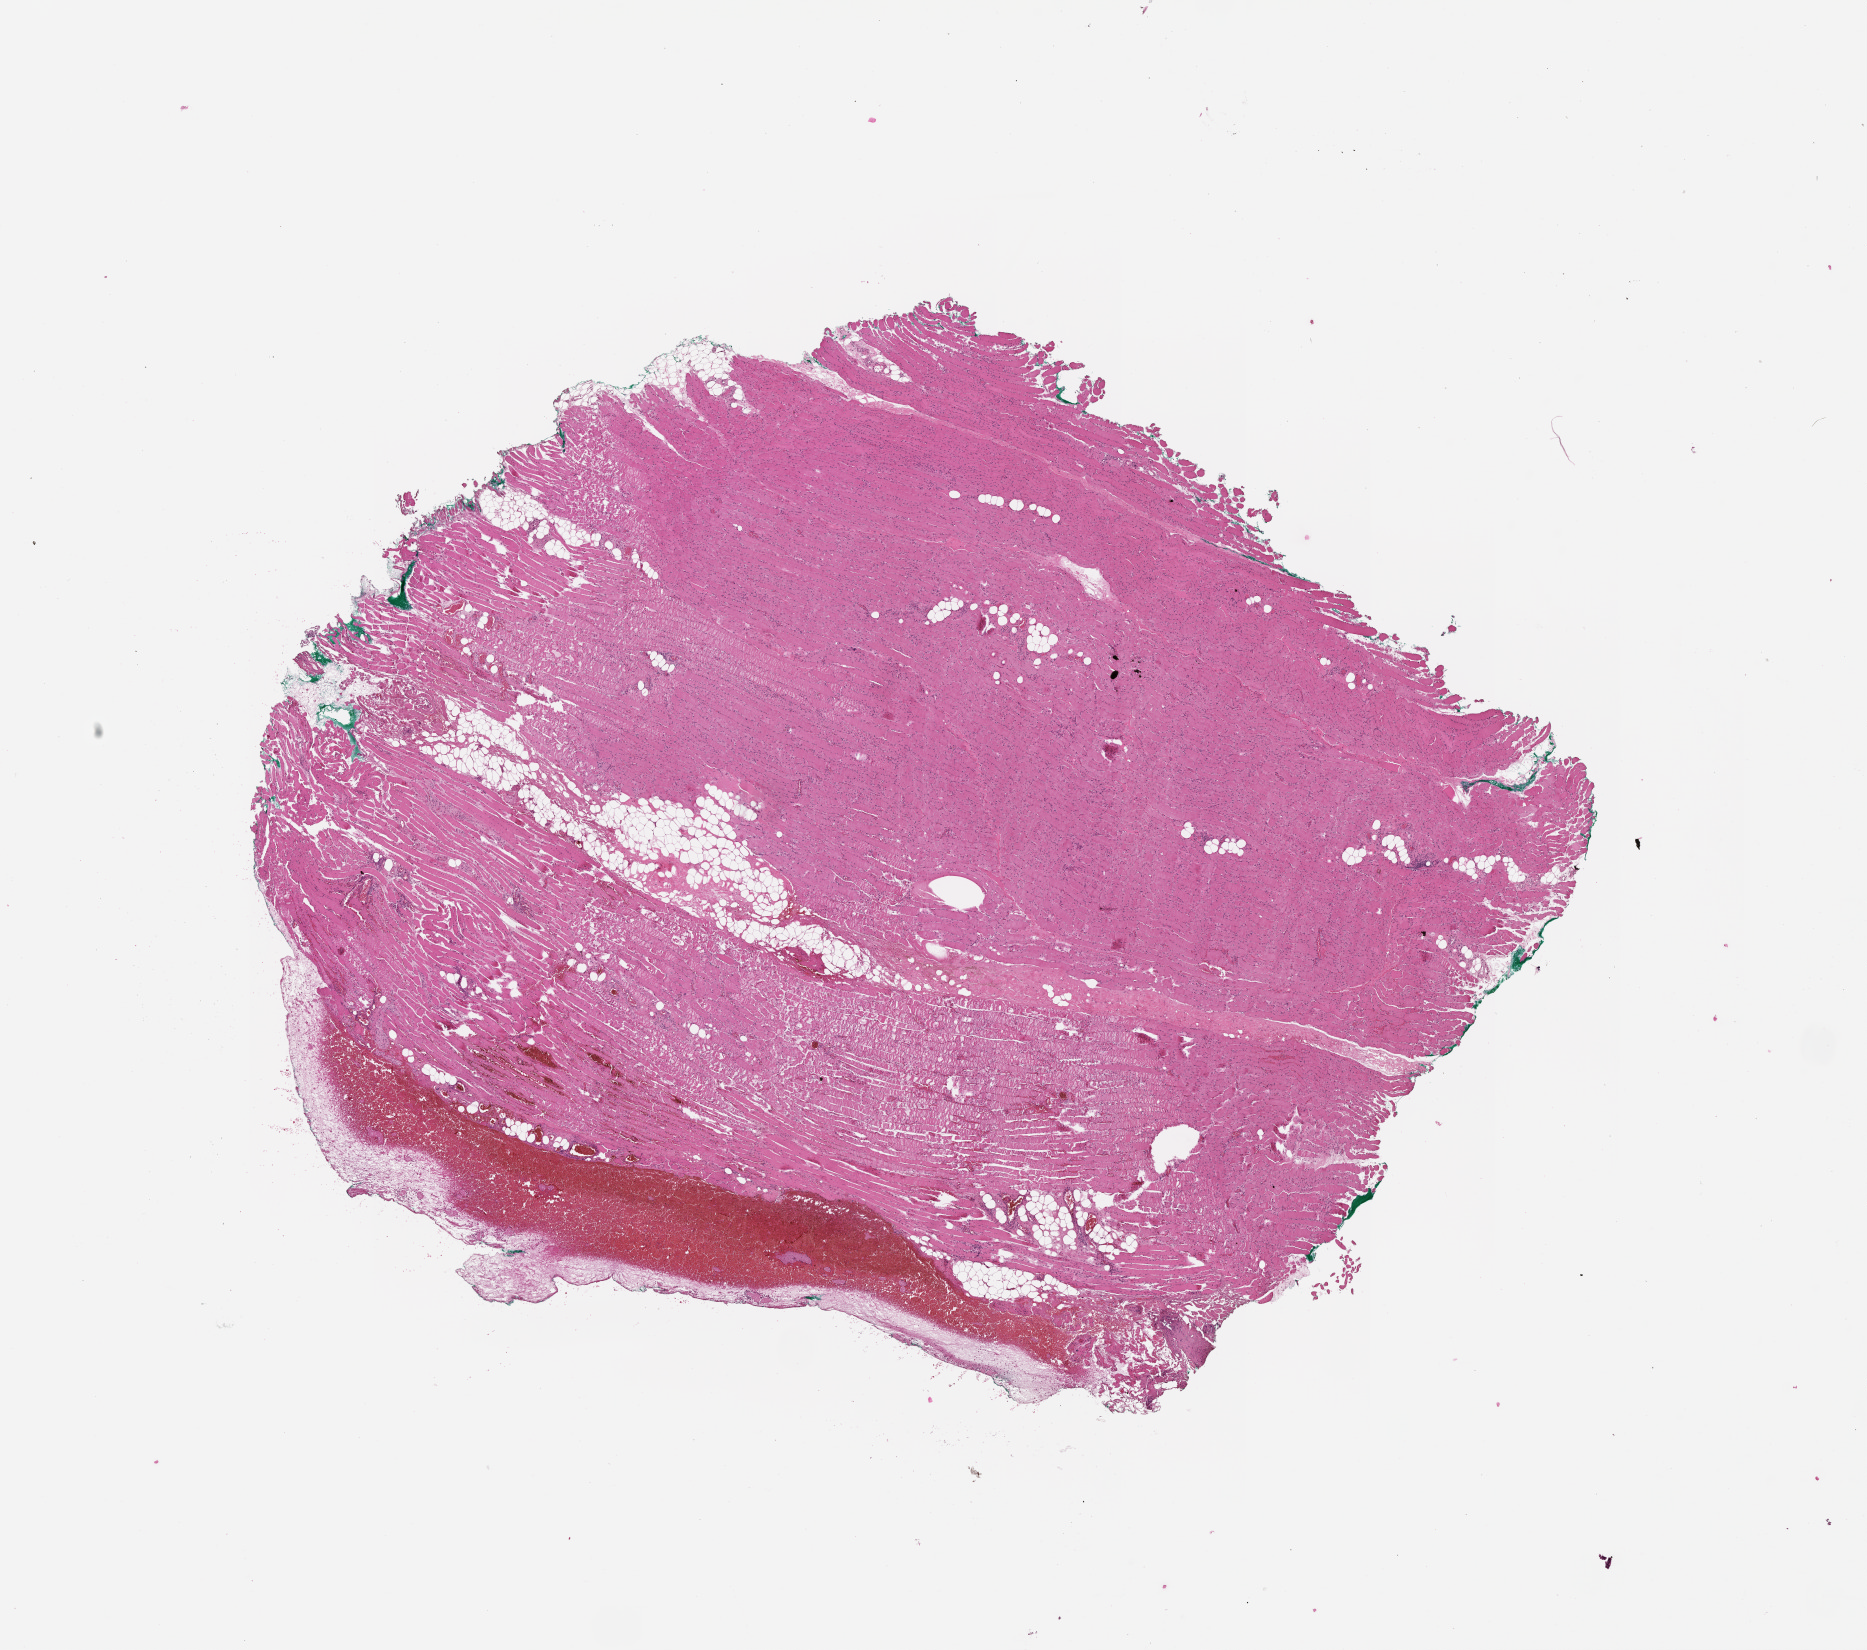
Digitized Hematoxylin and eosin (H&E) stained tissue section (whole slide), shown as a low-resolution overview of the whole scanned area (about 15.0 x 13.3 mm).
Patient diagnosis (cohort enrolment): sarcoma (site not recorded at cohort level).